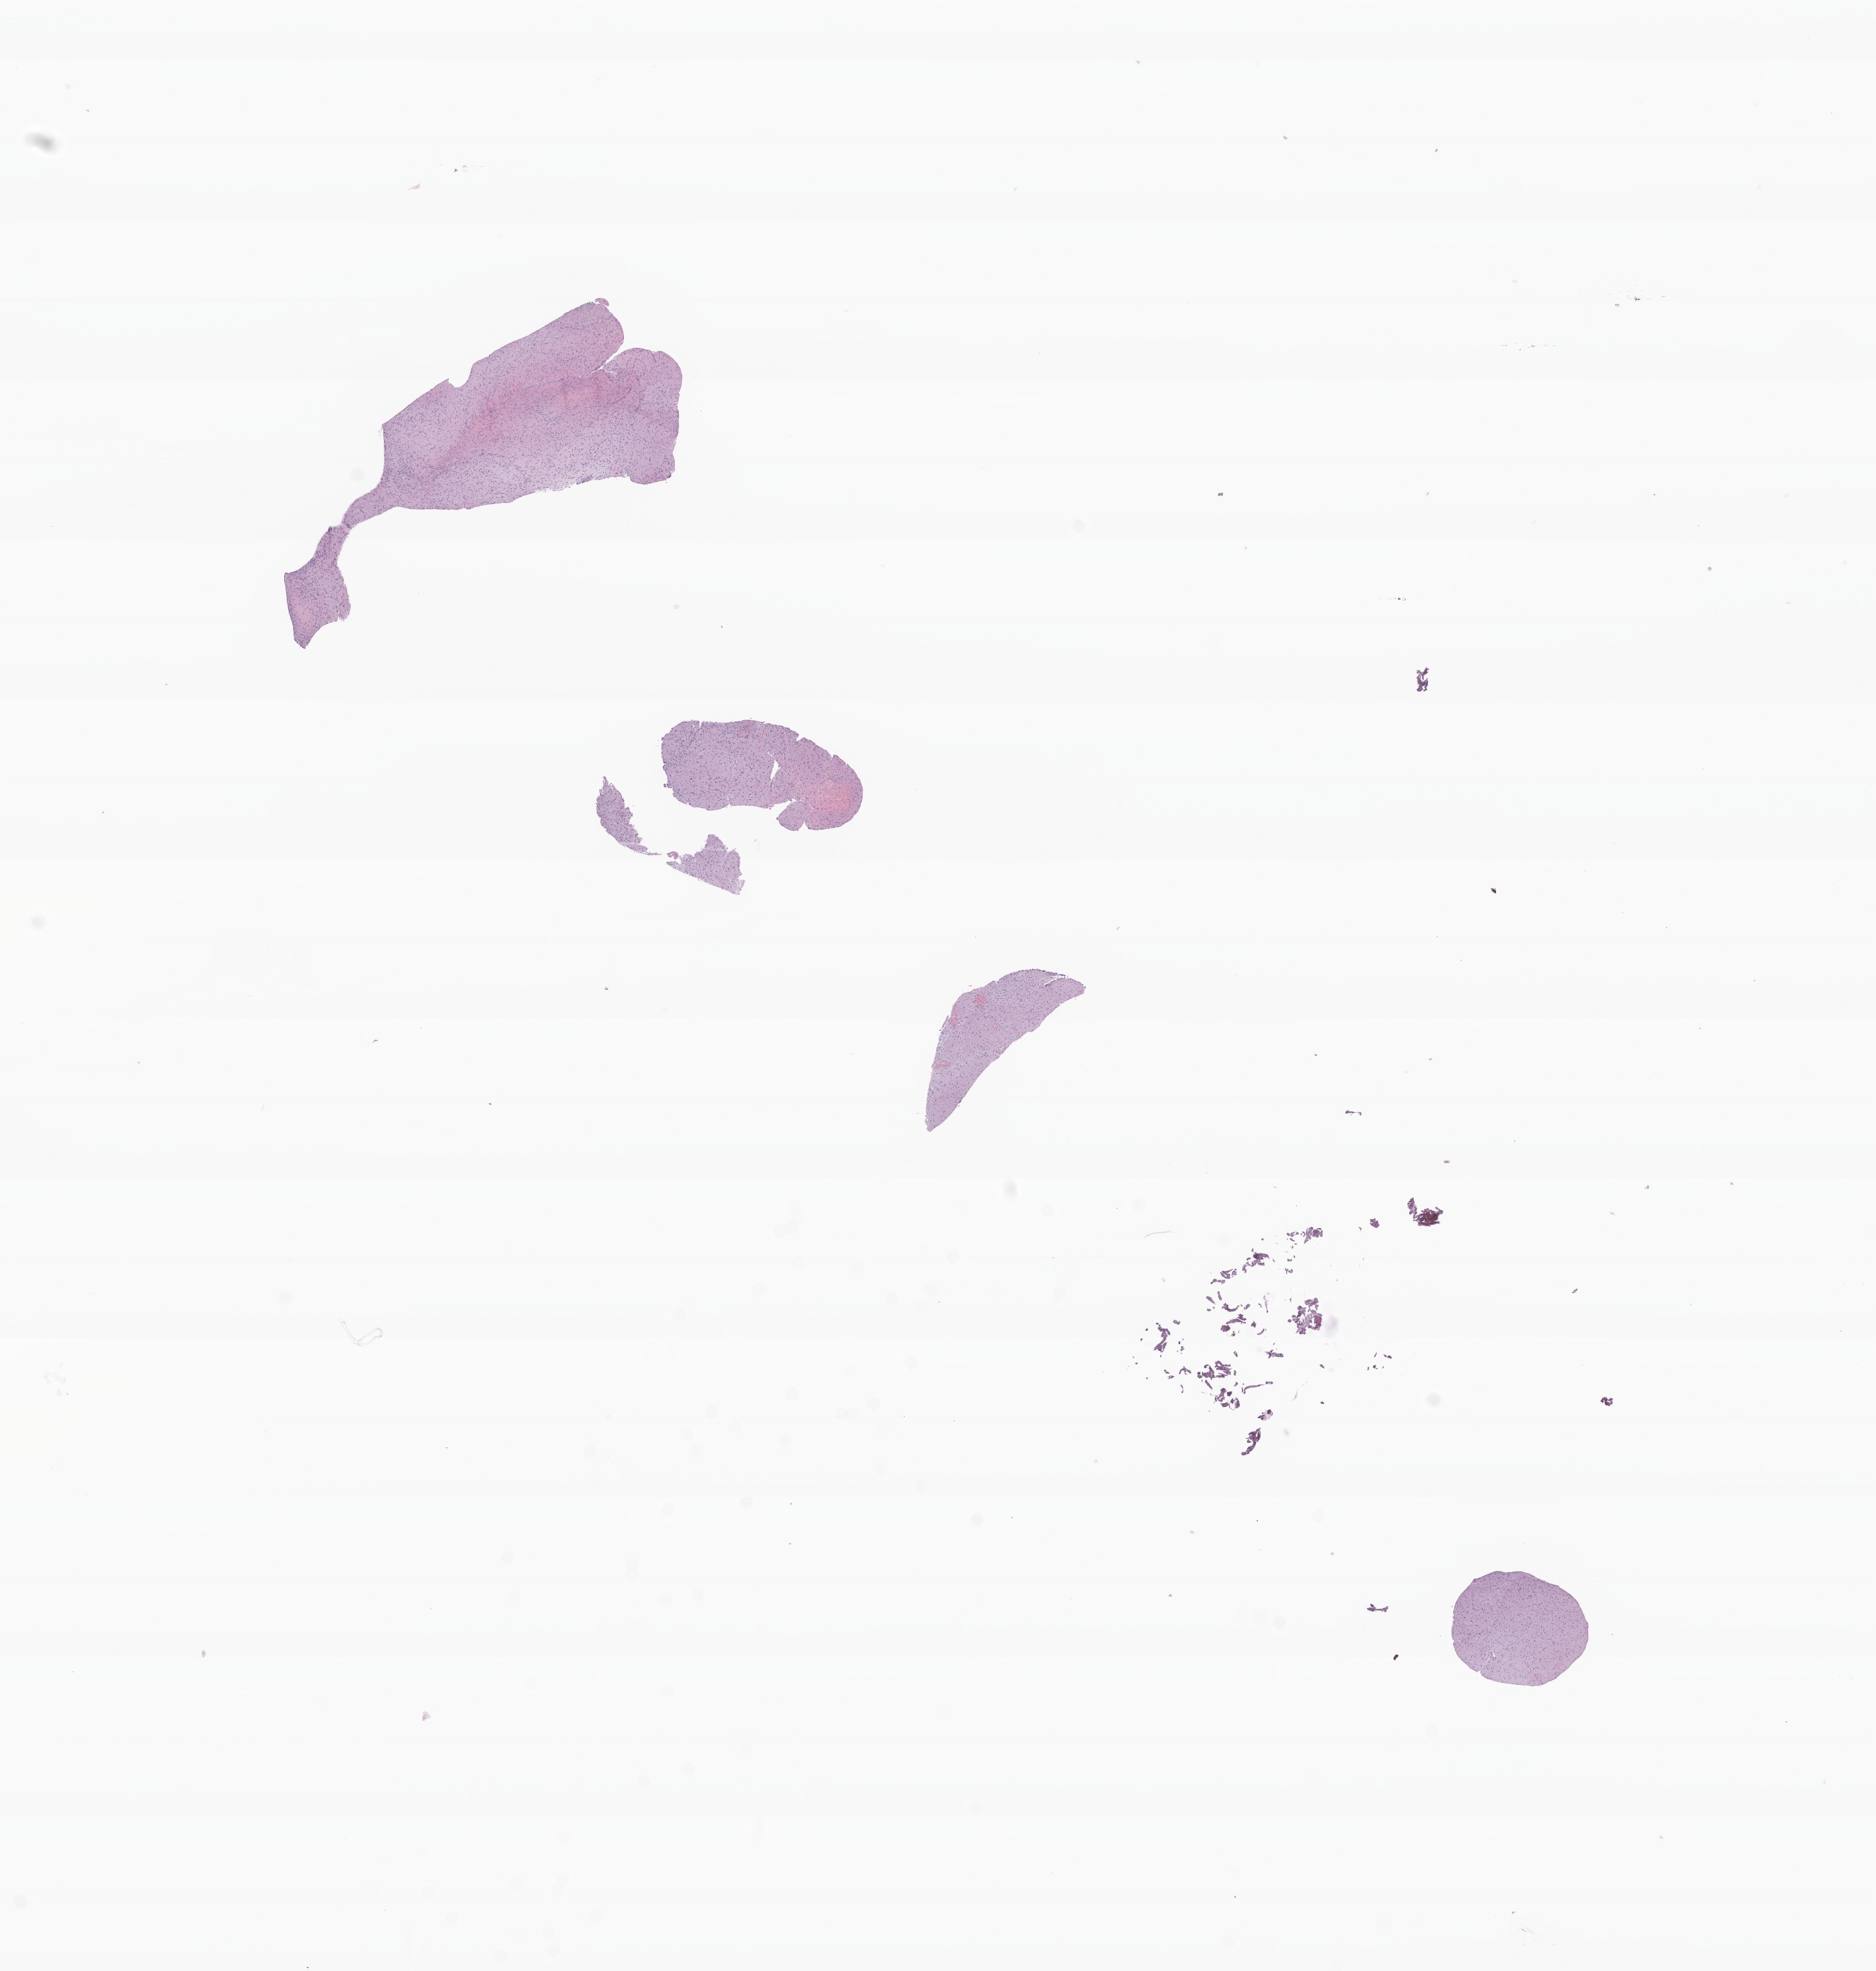
Digitized hematoxylin and eosin (H&E)-stained section of tumor tissue from the brain, whole scanned area (about 12.5 x 13.2 mm) shown as a low-resolution overview; formalin-fixed paraffin-embedded section. Patient female; age 109 months (9 years 1 month).
- diagnosis: Pilocytic astrocytoma